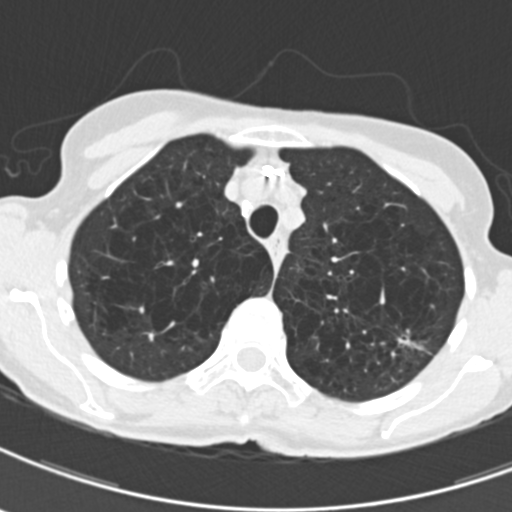
Low-dose screening chest CT, one axial slice; slice 157 of 203 in the series (ordered by position); reconstruction kernel B30f; lung window (W 1500 / L -600 HU); 512 × 512 image matrix, field of view 279 × 279 mm.
Structures marked on this image (expert manual segmentation):
- lesion 1 (tumor, upper lobe of left lung): bounding box (x1, y1, x2, y2) in pixels: (397, 336, 424, 351)